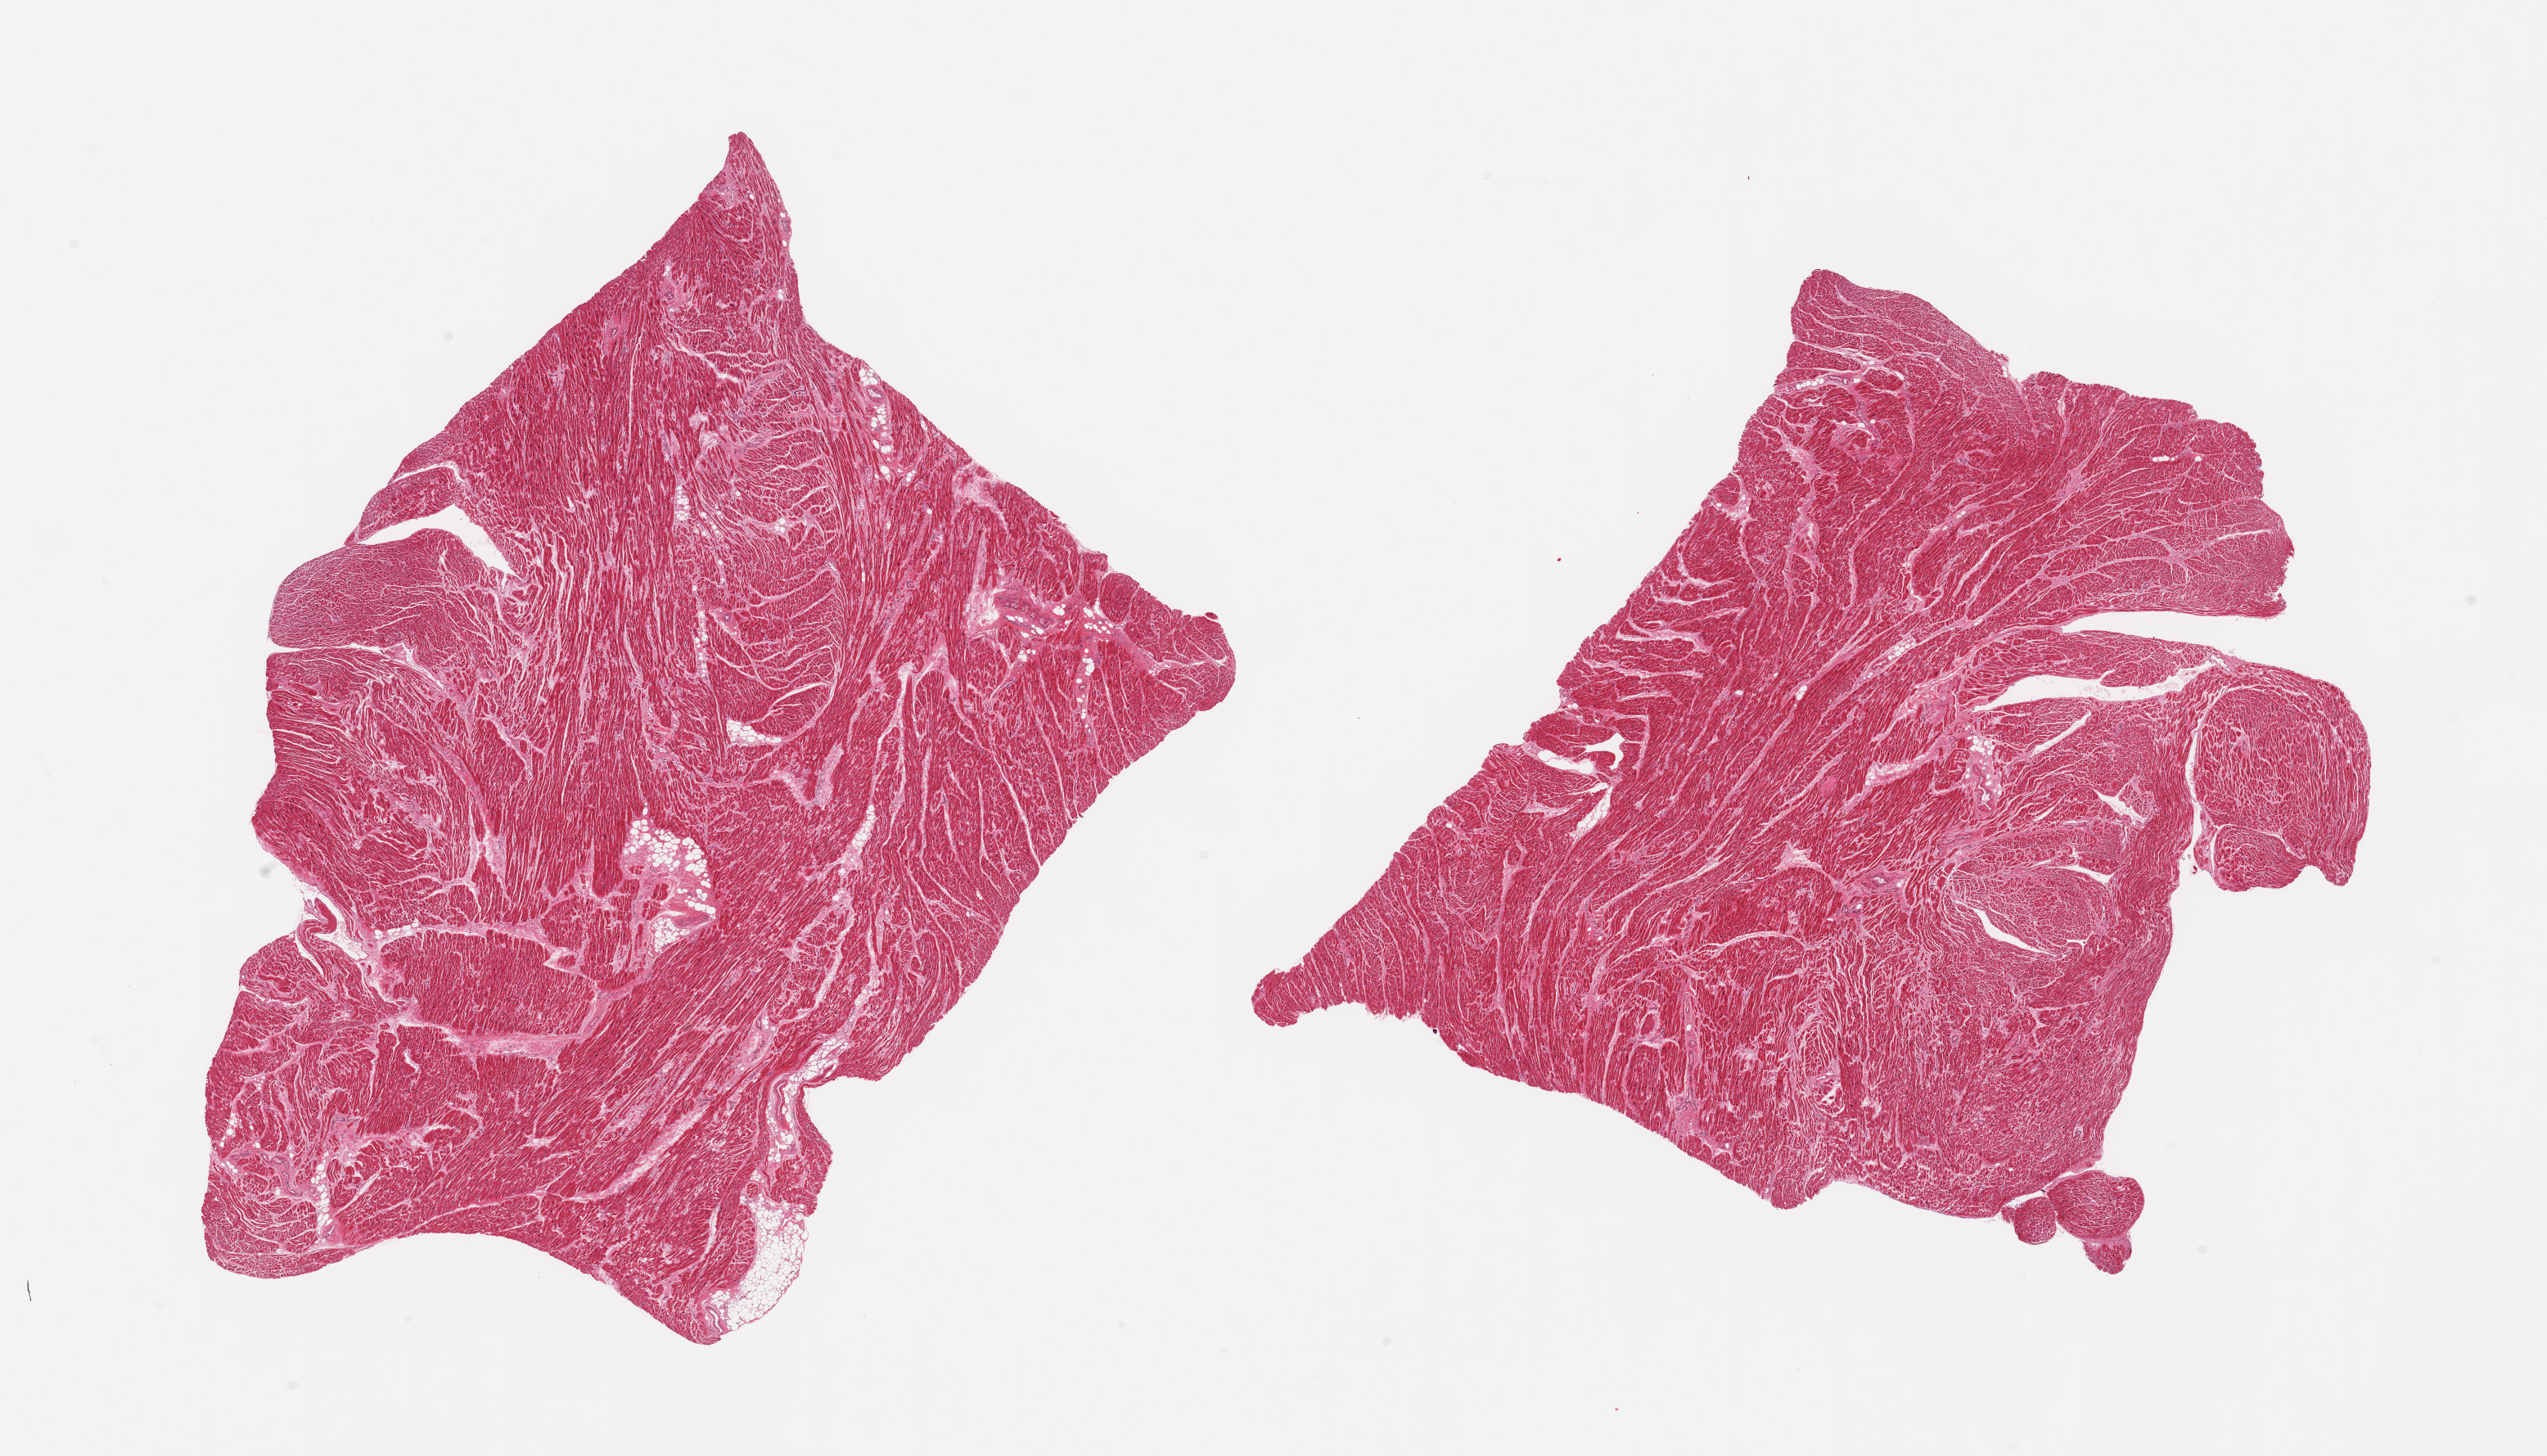
Whole-slide image, H&E stain — low-resolution overview of the scanned area, about 24.6 x 14.1 mm (from a 20x scan); PAXgene-fixed paraffin-embedded (PFPE) section; section of heart (target tissue); tissue donor sample. Donor sex: male.
* reviewer comment on this tissue sample: 2 pieces; mild interstitial fibrosis